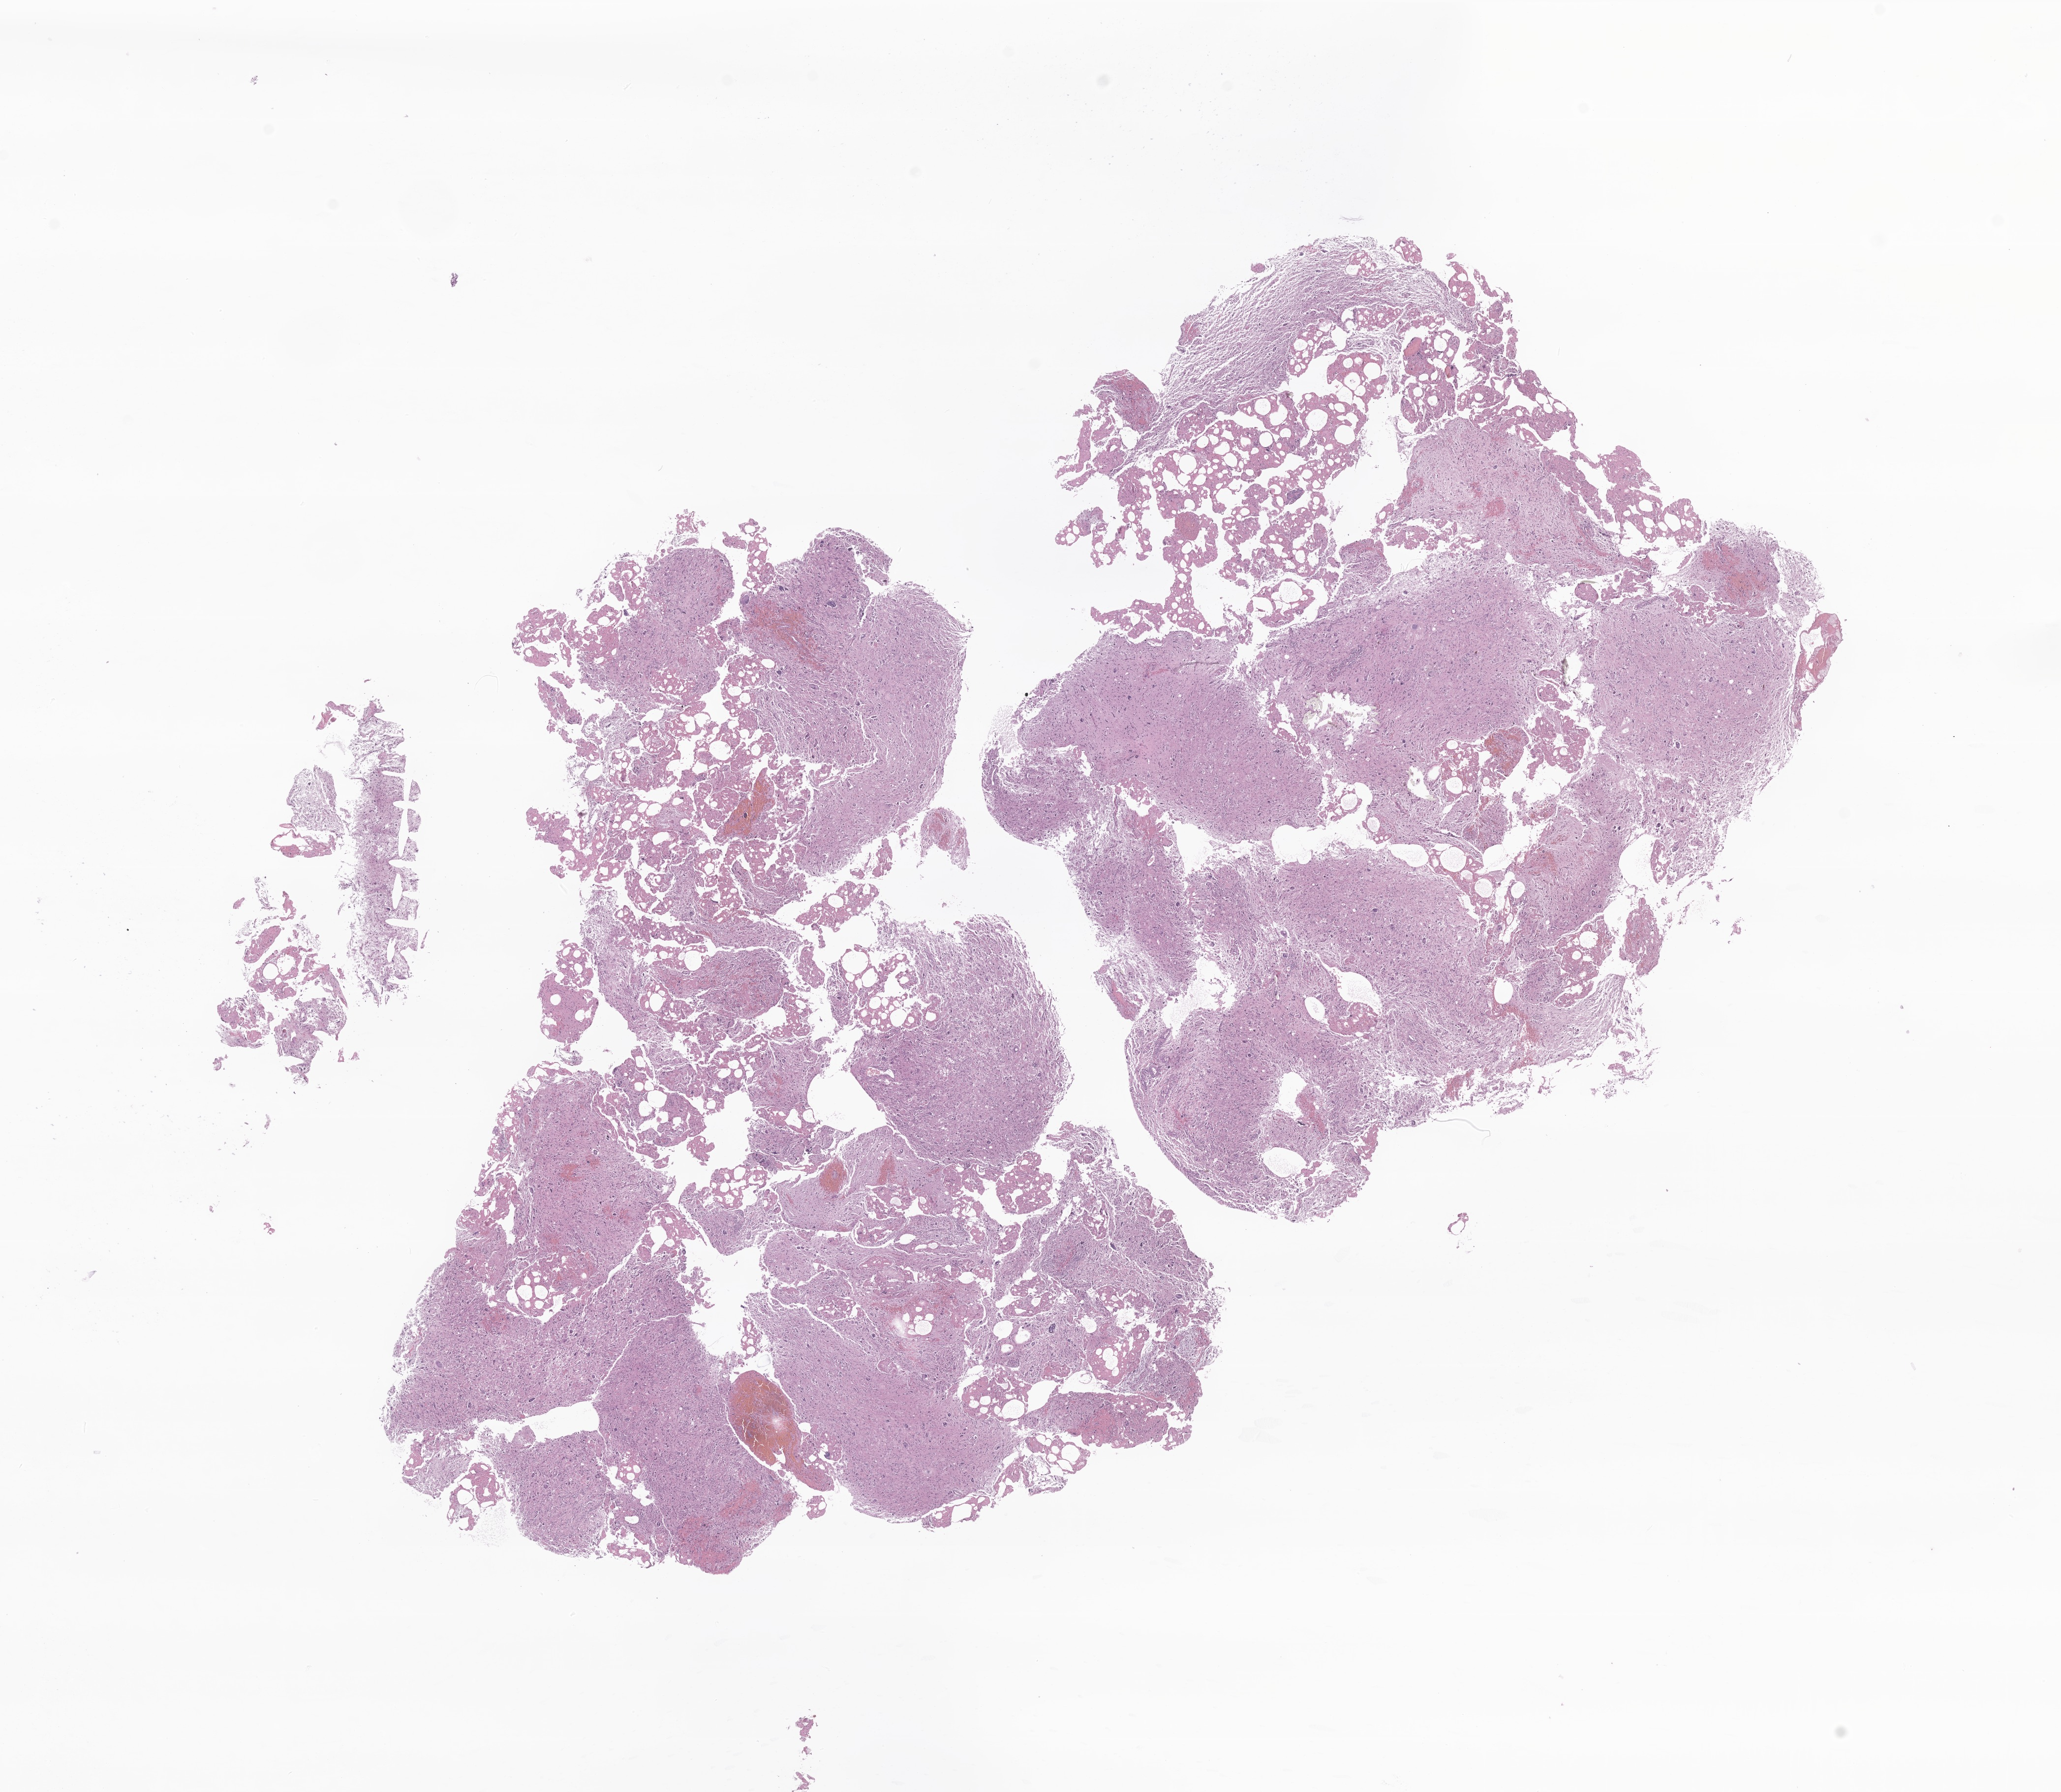
Digitized hematoxylin and eosin (H&E)-stained section of tumor tissue from the brain stem — whole scanned area (about 17.7 x 15.4 mm) shown as a low-resolution overview; formalin-fixed paraffin-embedded section. Patient: female, age 143 months (11 years 11 months).
Diagnosis: Astrocytoma, NOS.